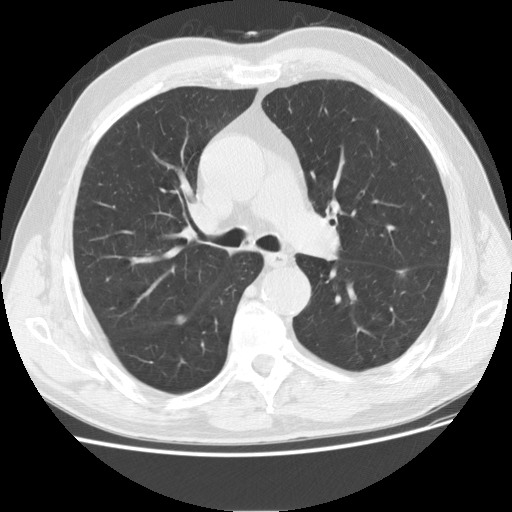
Low-dose screening chest CT, one axial slice. Lung window (W 1500 / L -600 HU). 2.5 mm slice thickness. 512 × 512 image matrix, field of view 360 × 360 mm.
Outlined on this slice (outlined manually by an expert reader):
- lesion 1 (tumor, lower lobe of left lung): box from (x=396, y=268) to (x=407, y=278) px